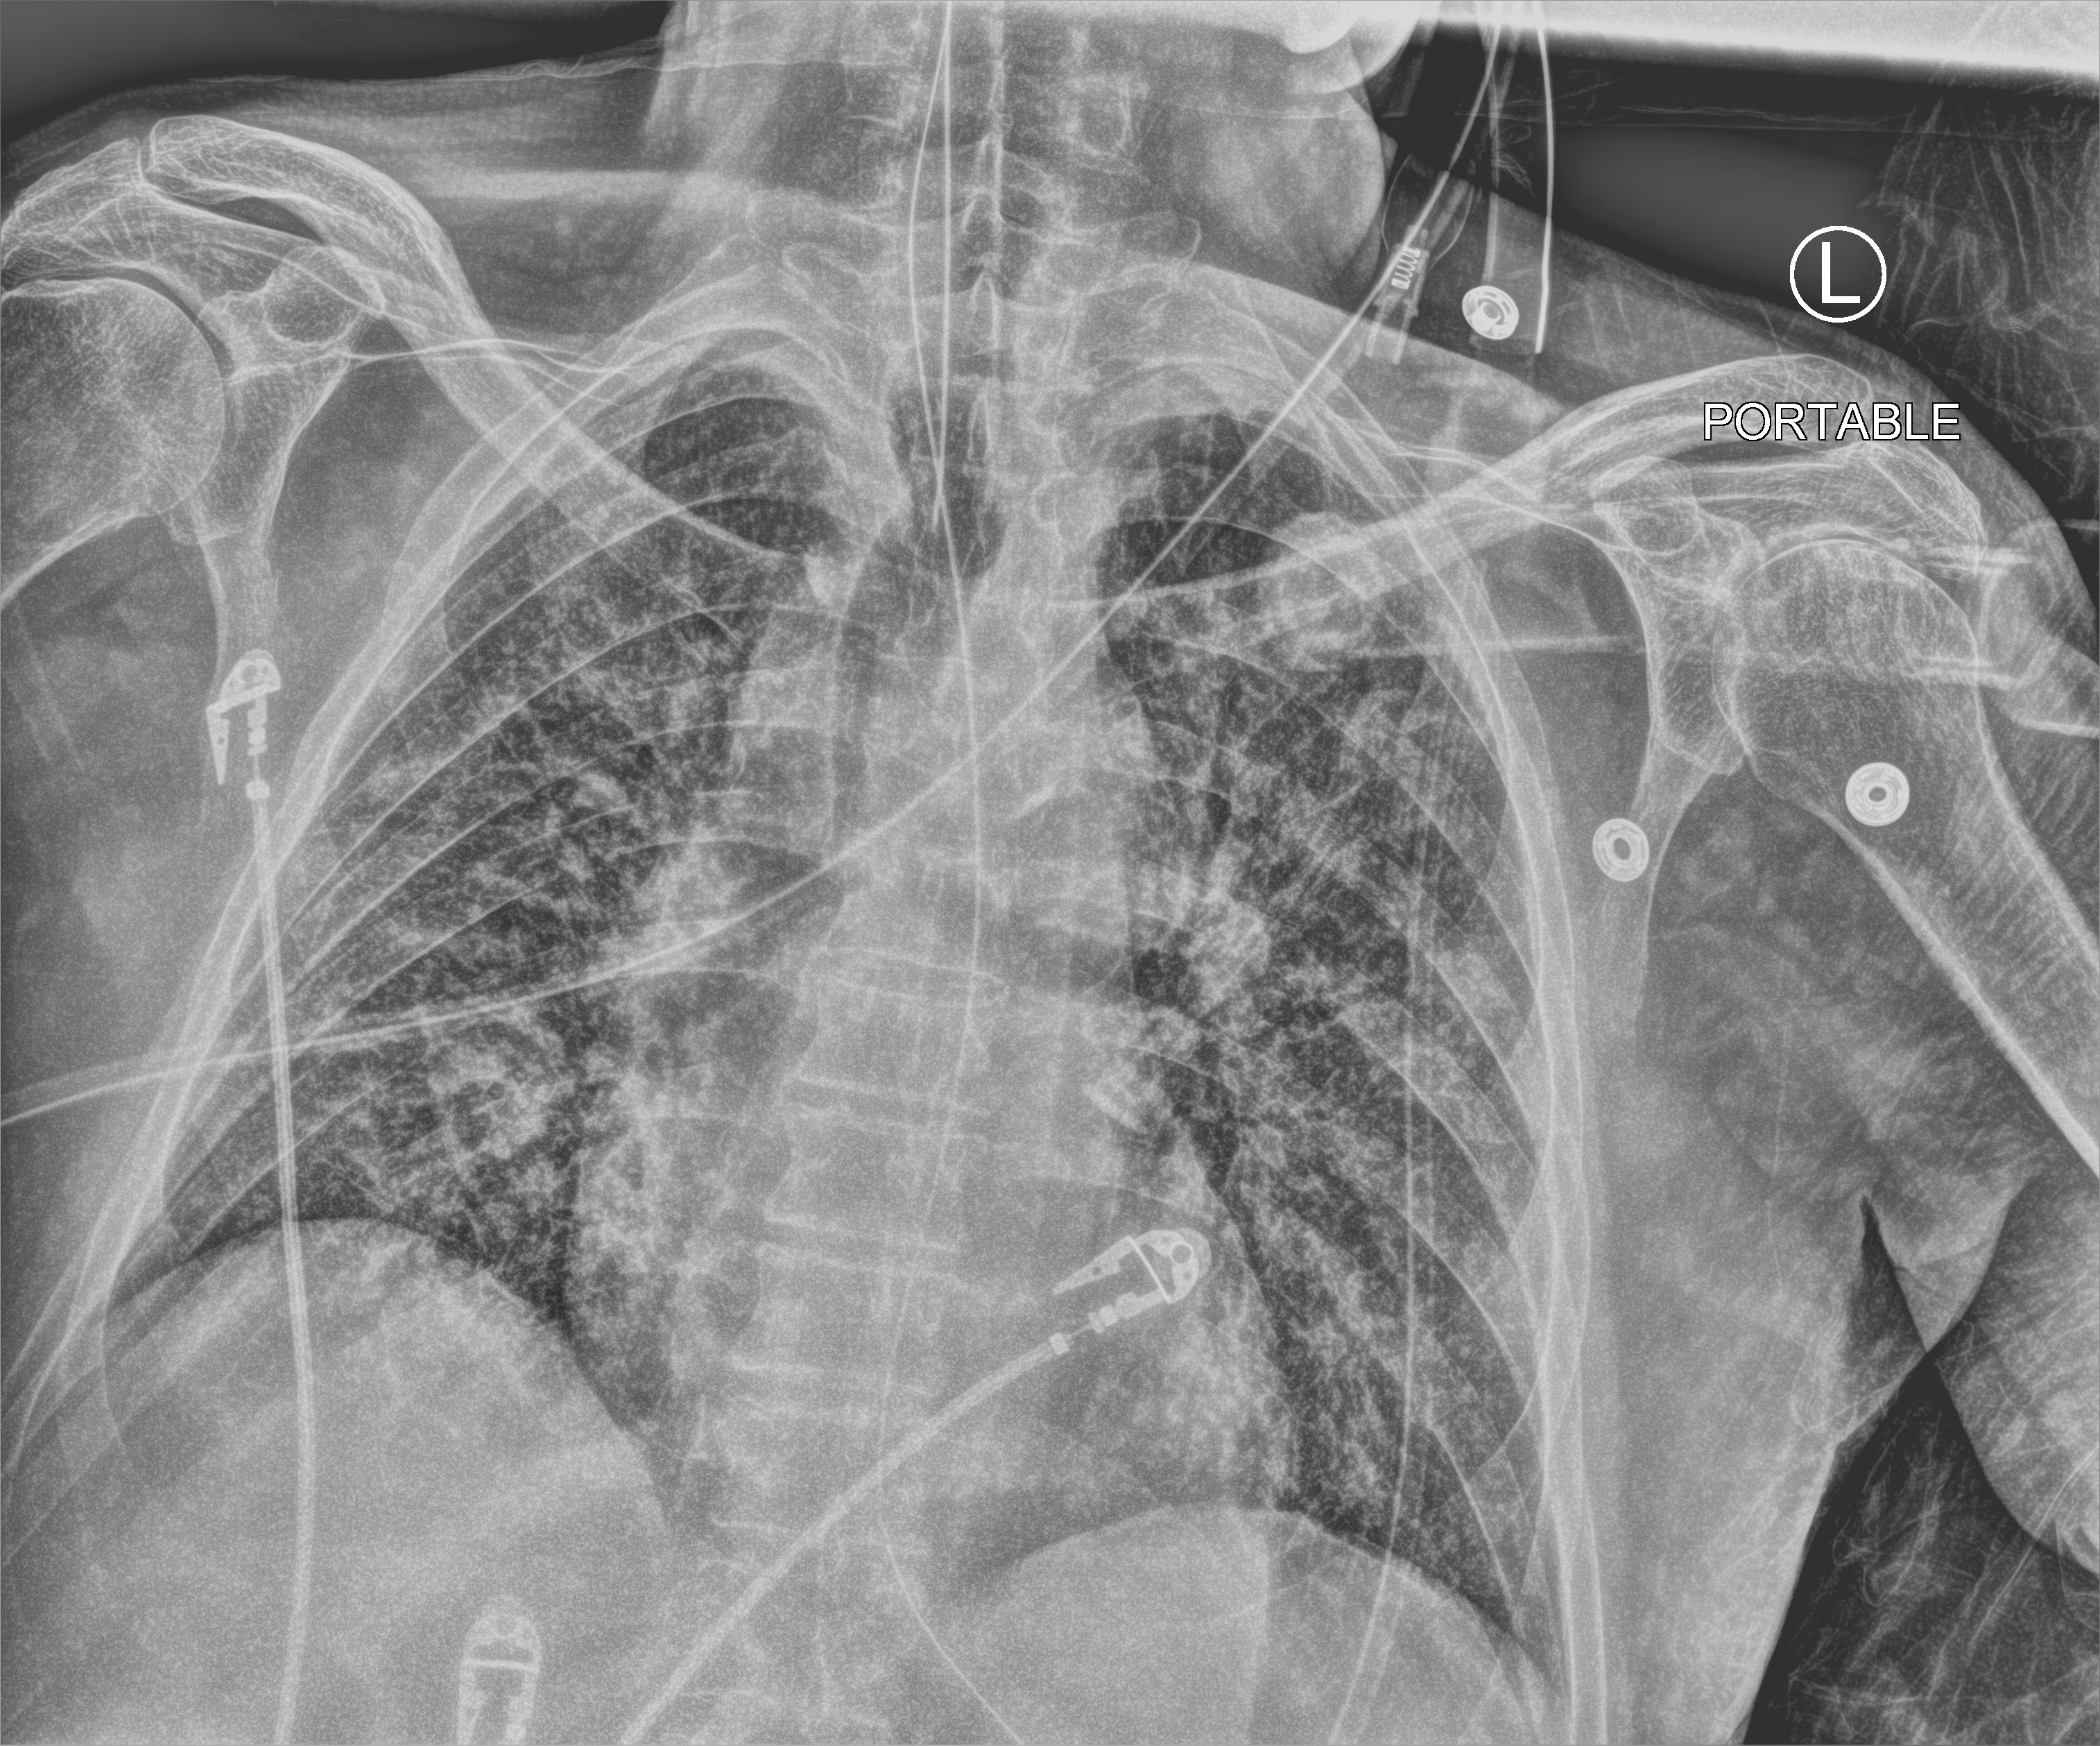
Chest X-ray (portable), anteroposterior (AP) projection. Male patient hospitalised with COVID-19, age 60–74 years.
From the hospital-stay record, not from the radiograph (when in the stay this image was taken is not recorded):
- admitted to intensive care during this hospital stay: yes
- chronic kidney disease (admission record): no
- mechanically ventilated during this hospital stay: yes